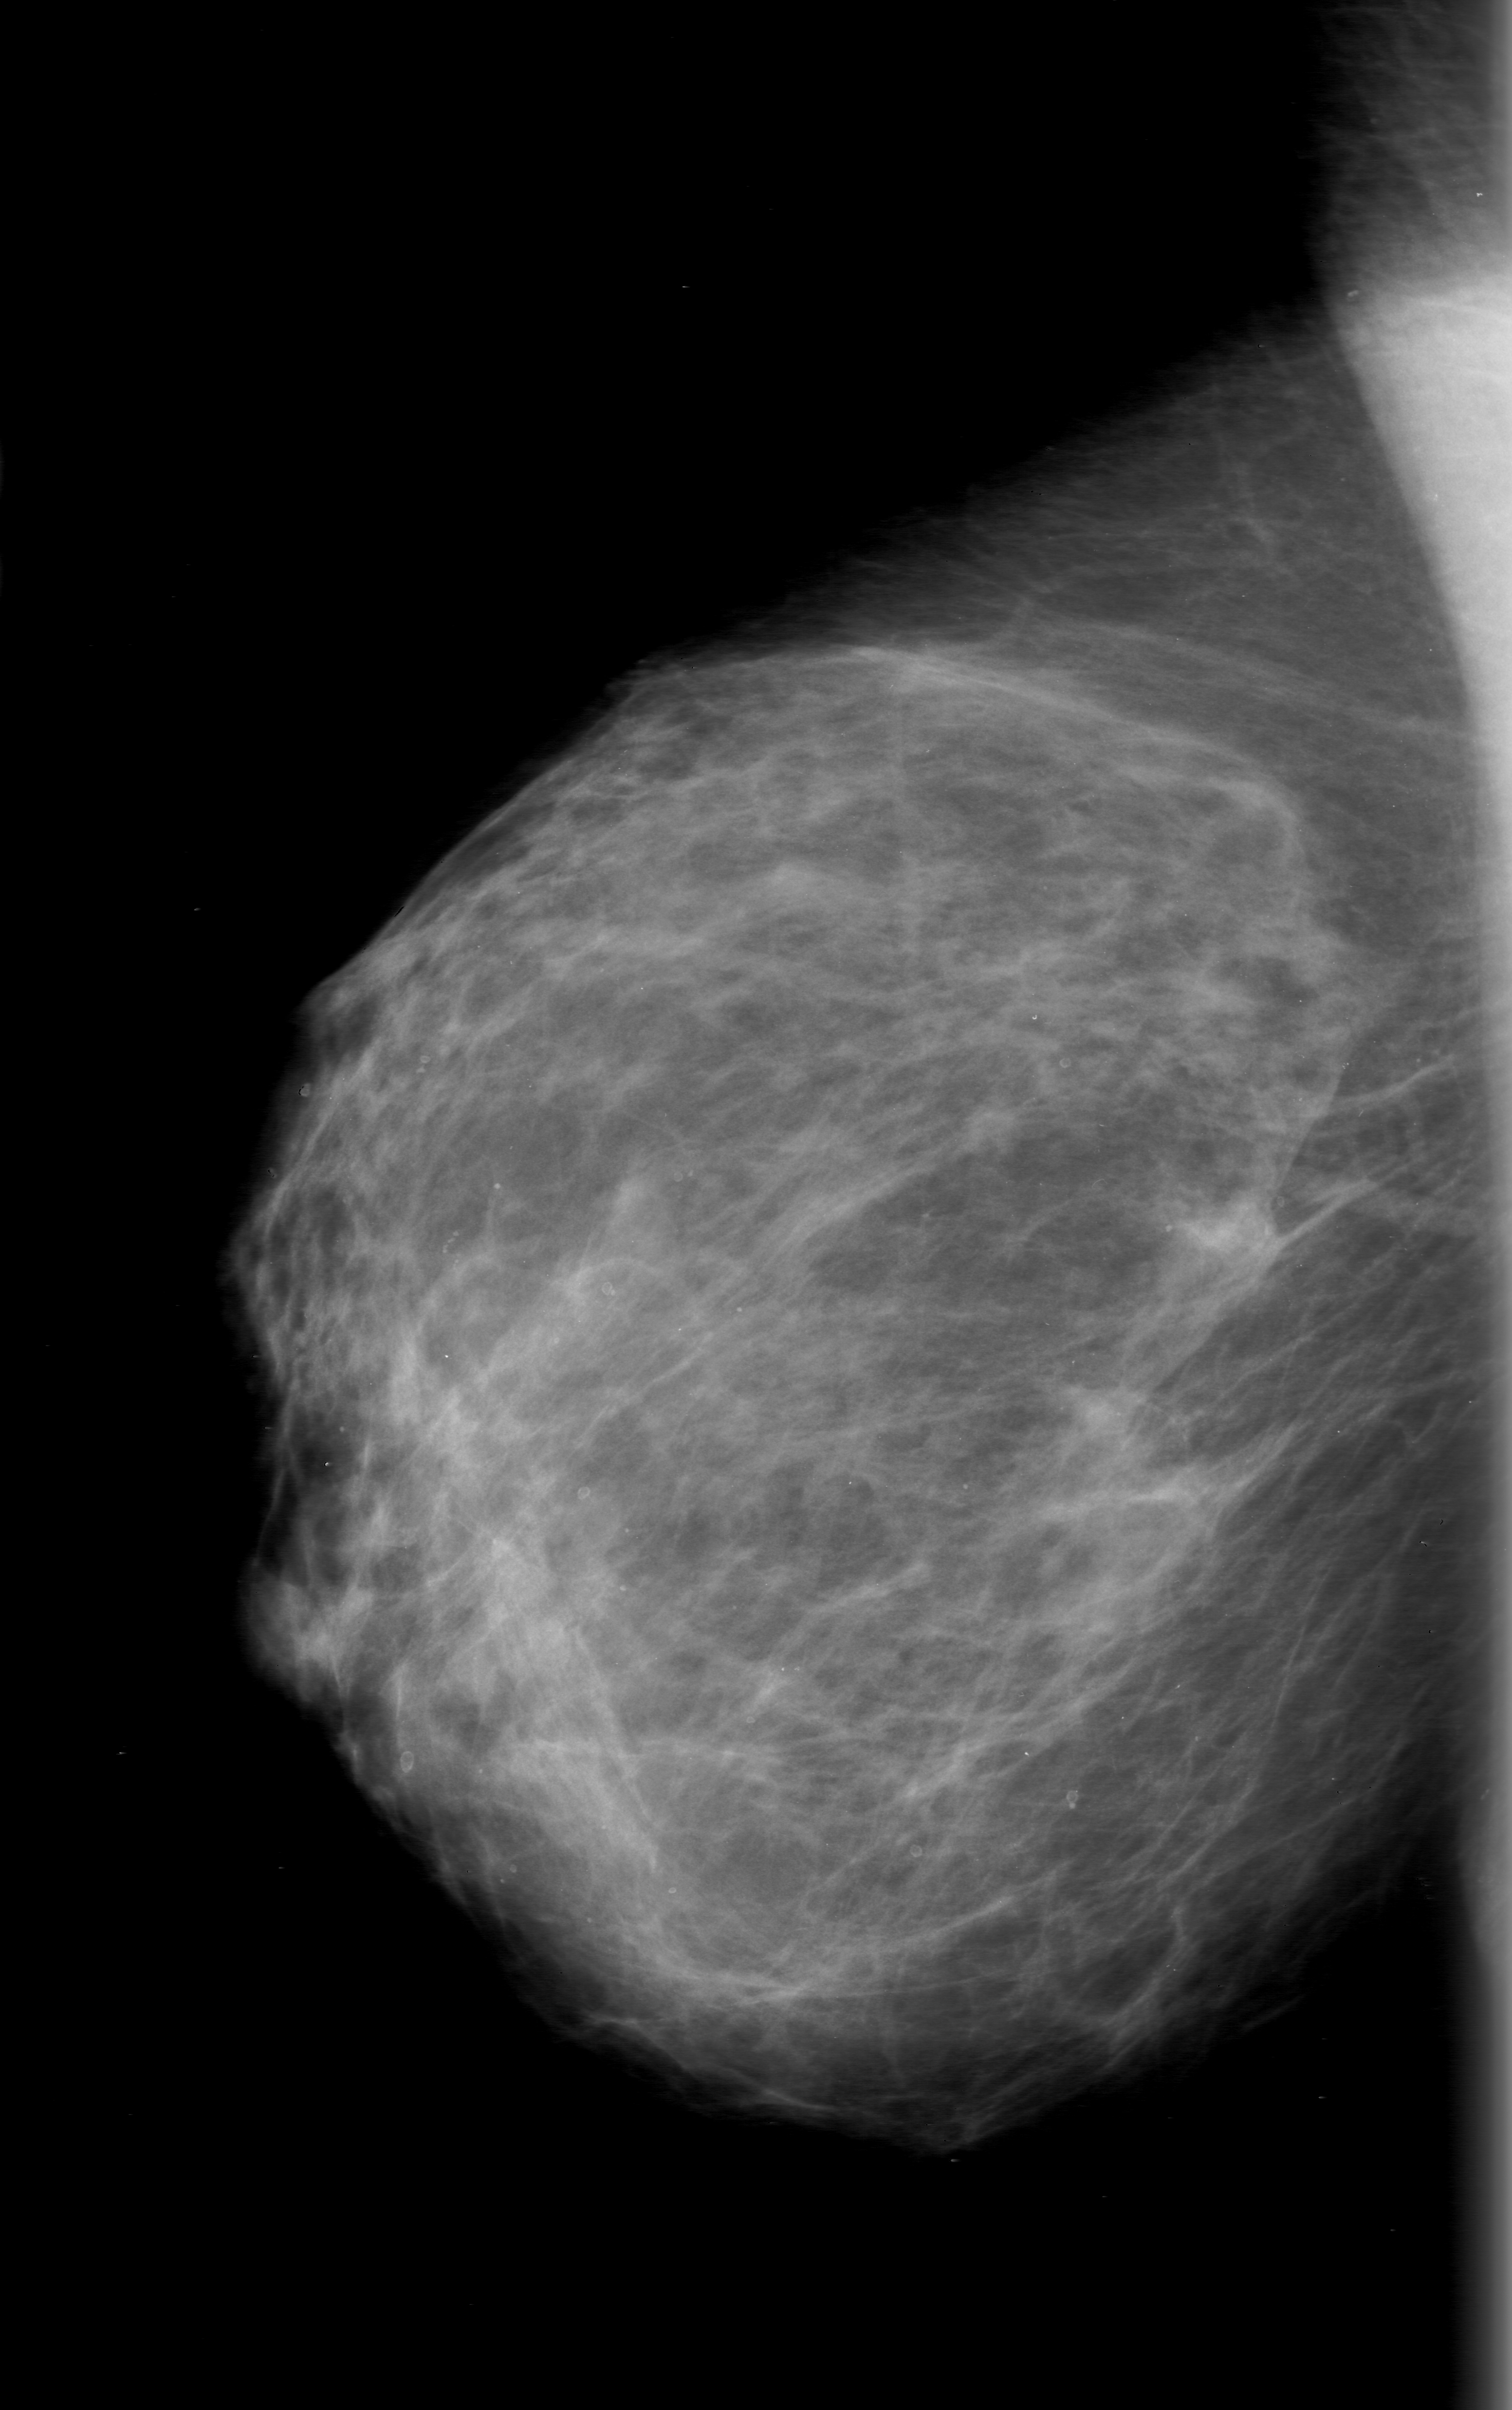
Digitized screen-film mammogram, right breast, MLO view, BI-RADS breast density category 2 (scale 1–4).
- Abnormality record for this image: mass, shape architectural distortion; BI-RADS assessment category 0 (incomplete: needs additional imaging); subtlety rating 4 on a 1 (subtle) to 5 (obvious) scale; pathology (as recorded): malignant.